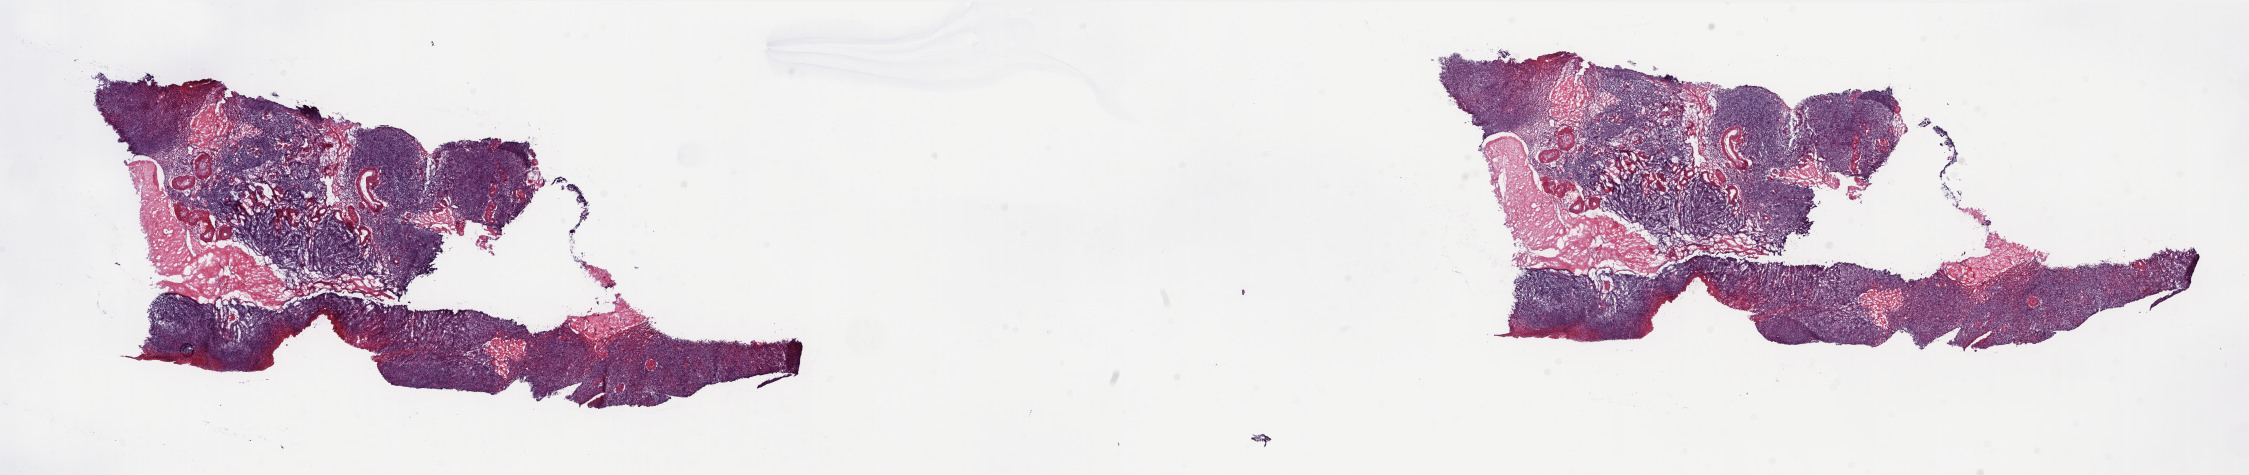
Hematoxylin and eosin (H&E) stained whole-slide image — whole scanned area (about 35.9 x 7.6 mm, slide scanned at 20x) shown as a low-resolution overview, frozen section from the top of the tissue portion, sample: solid tissue normal (non-tumour tissue), uterus. Female, age 74 years at initial diagnosis. Composition of this section per pathologist review: tumour cells 0%, tumour nuclei 0%, normal cells 100%, stromal cells 0%, necrosis 0%. Inflammatory infiltration, as recorded: lymphocyte infiltration 0%, monocyte infiltration 0%, neutrophil infiltration 0%.
This section: solid tissue normal sample (biorepository sample class). Patient diagnosis: Endometrioid adenocarcinoma, NOS (endometrium).